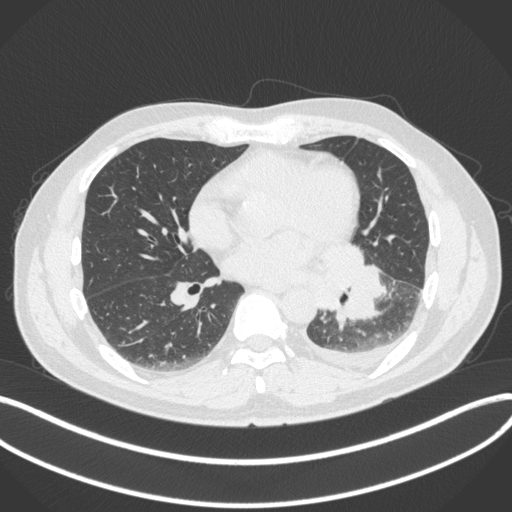
Chest CT, one axial slice. Position 161 of 350 along the scan axis. Reconstruction kernel B31f. 120 kVp. Lung window (W 1500 / L -600 HU). 512 × 512 image matrix. Male patient, age 58 years. Case-level facts recorded for this patient, not image findings: clinical TNM (as recorded): T3 N1 M1b; histopathological grade: G3.
Annotated regions visible in this slice (rectangle marked by the reading radiologist):
- lung tumour (recorded histology: small cell carcinoma): bounding box <305,243,390,324> (left, top, right, bottom; pixels)